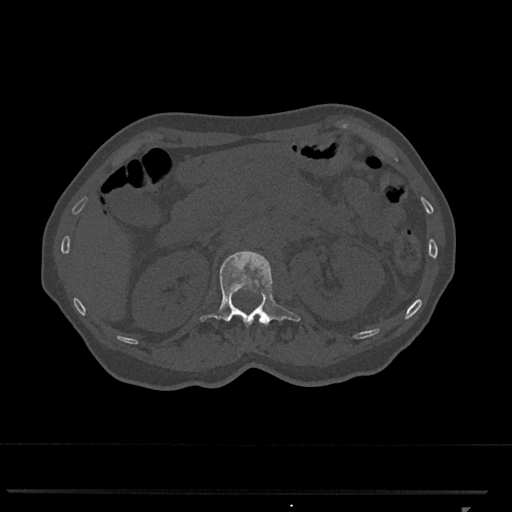
CT including the spine, one axial slice. Position 407 of 793 along the scan axis. 120 kVp. Bone window (W 1800 / L 400 HU). 0.5 mm slice thickness. 512 × 512 image matrix, field of view 380 × 380 mm. Female patient, age 62 years. Case-level facts recorded for this patient, not image findings: primary cancer: renal.
Annotated regions visible in this slice (semi-automatic segmentation, software-assisted and operator-edited):
- L1 vertebra: bounding box <199,251,301,327> (left, top, right, bottom; pixels)